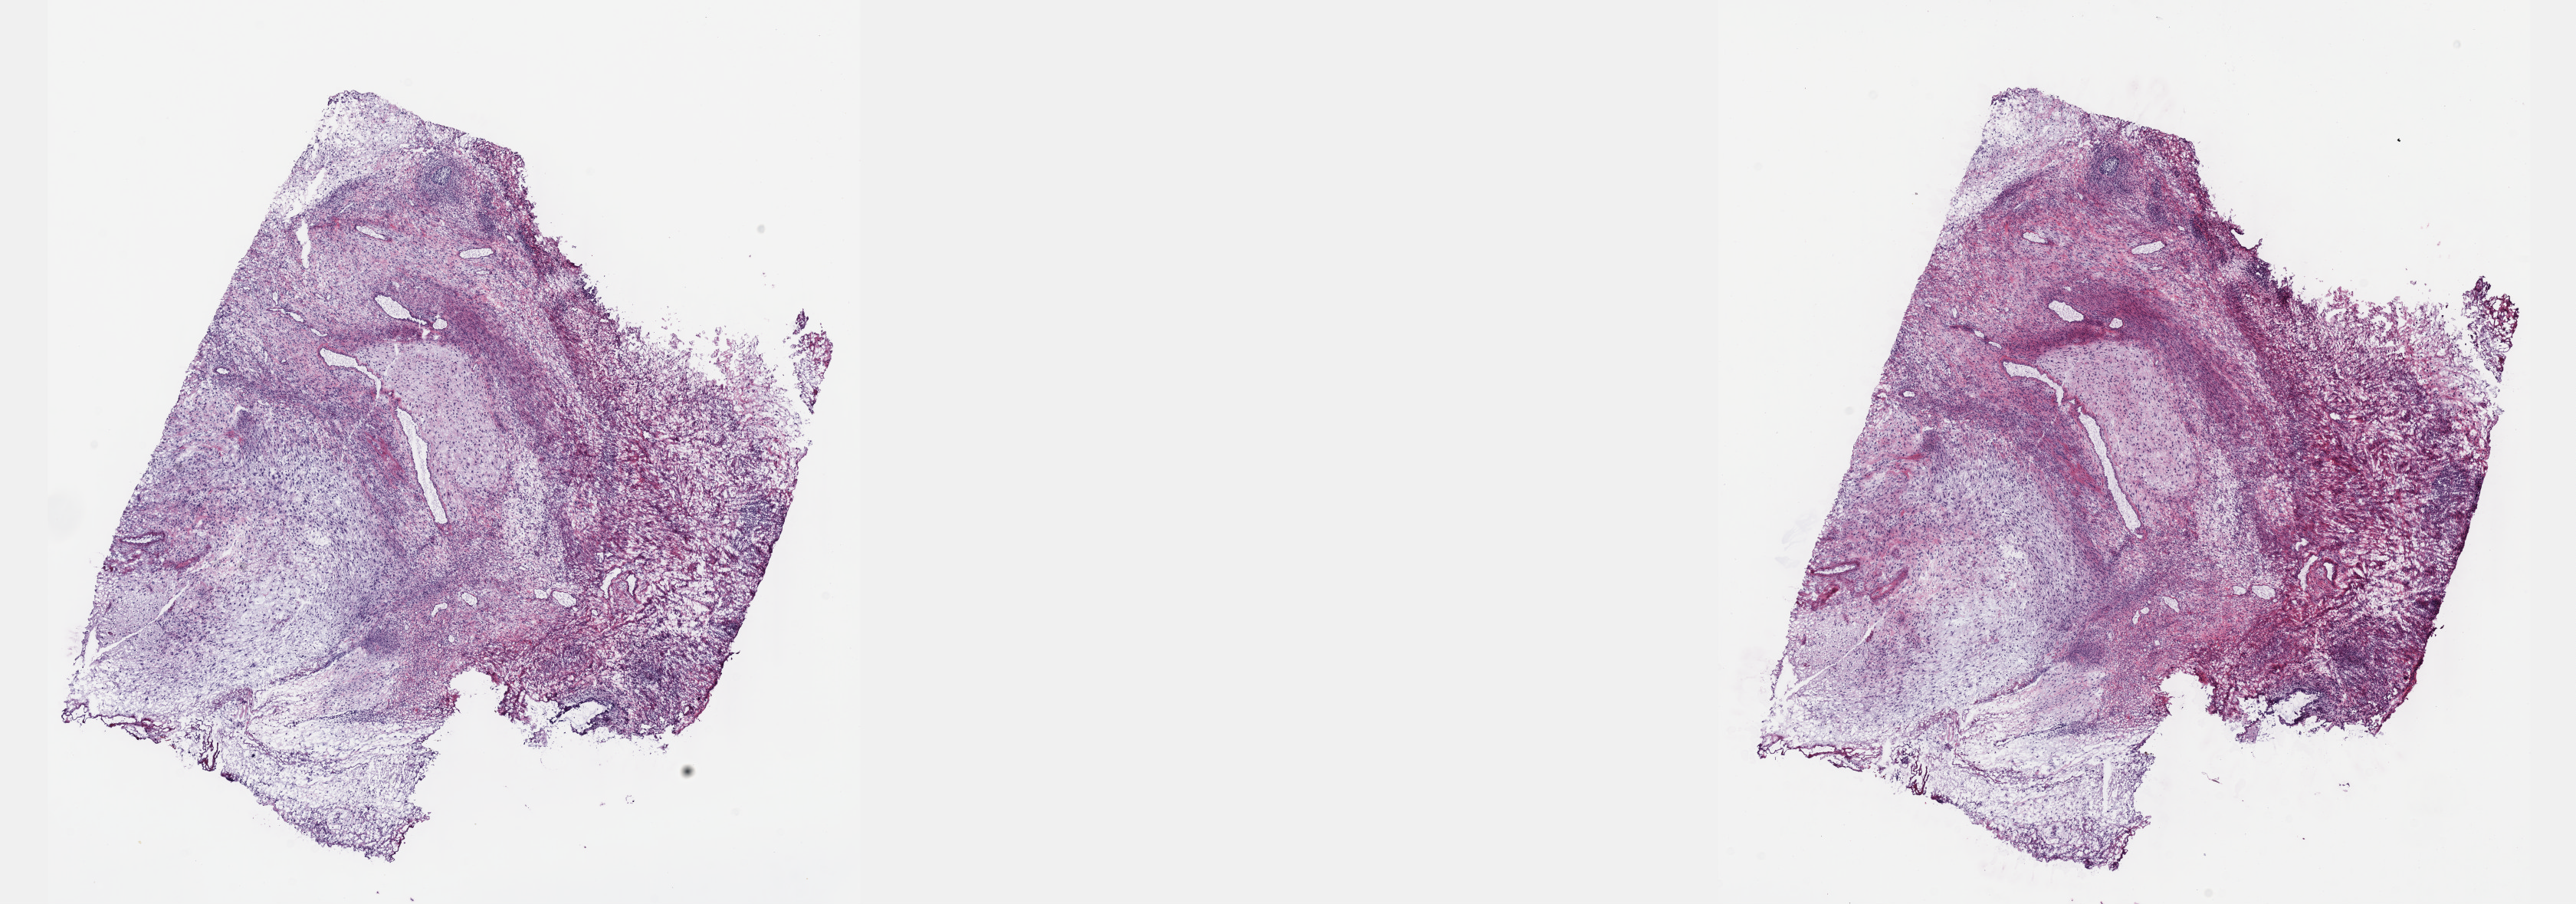
H&E-stained whole-slide image, a low-resolution overview of the entire scanned area, about 27.2 x 9.5 mm. Male patient. Composition of this section per pathologist review: tumour cells 90%, tumour nuclei 95%, normal cells 0%, stromal cells 10%, necrosis 0%. Inflammatory infiltration, as recorded: lymphocyte infiltration 0%, monocyte infiltration 0%, neutrophil infiltration 0%.
* specimen: frozen section from the top of the tissue portion; testis, primary tumour sample